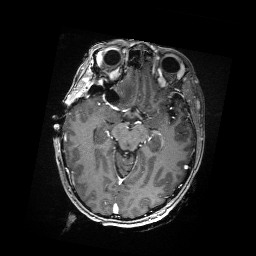
Brain MRI from a brain-tumour surgery series, one axial slice. Slice 105 of 176 in the series (ordered by position). T1-weighted post-contrast. 1 mm slice thickness. 256 × 256 image matrix, field of view 256 × 256 mm. Case-level facts recorded for this patient, not image findings: histopathology: Metastatic Carcinoma from Breast primary.
Structures marked on this image (outlined manually by an expert reader):
- residual tumour: box from (x=99, y=90) to (x=105, y=95) px